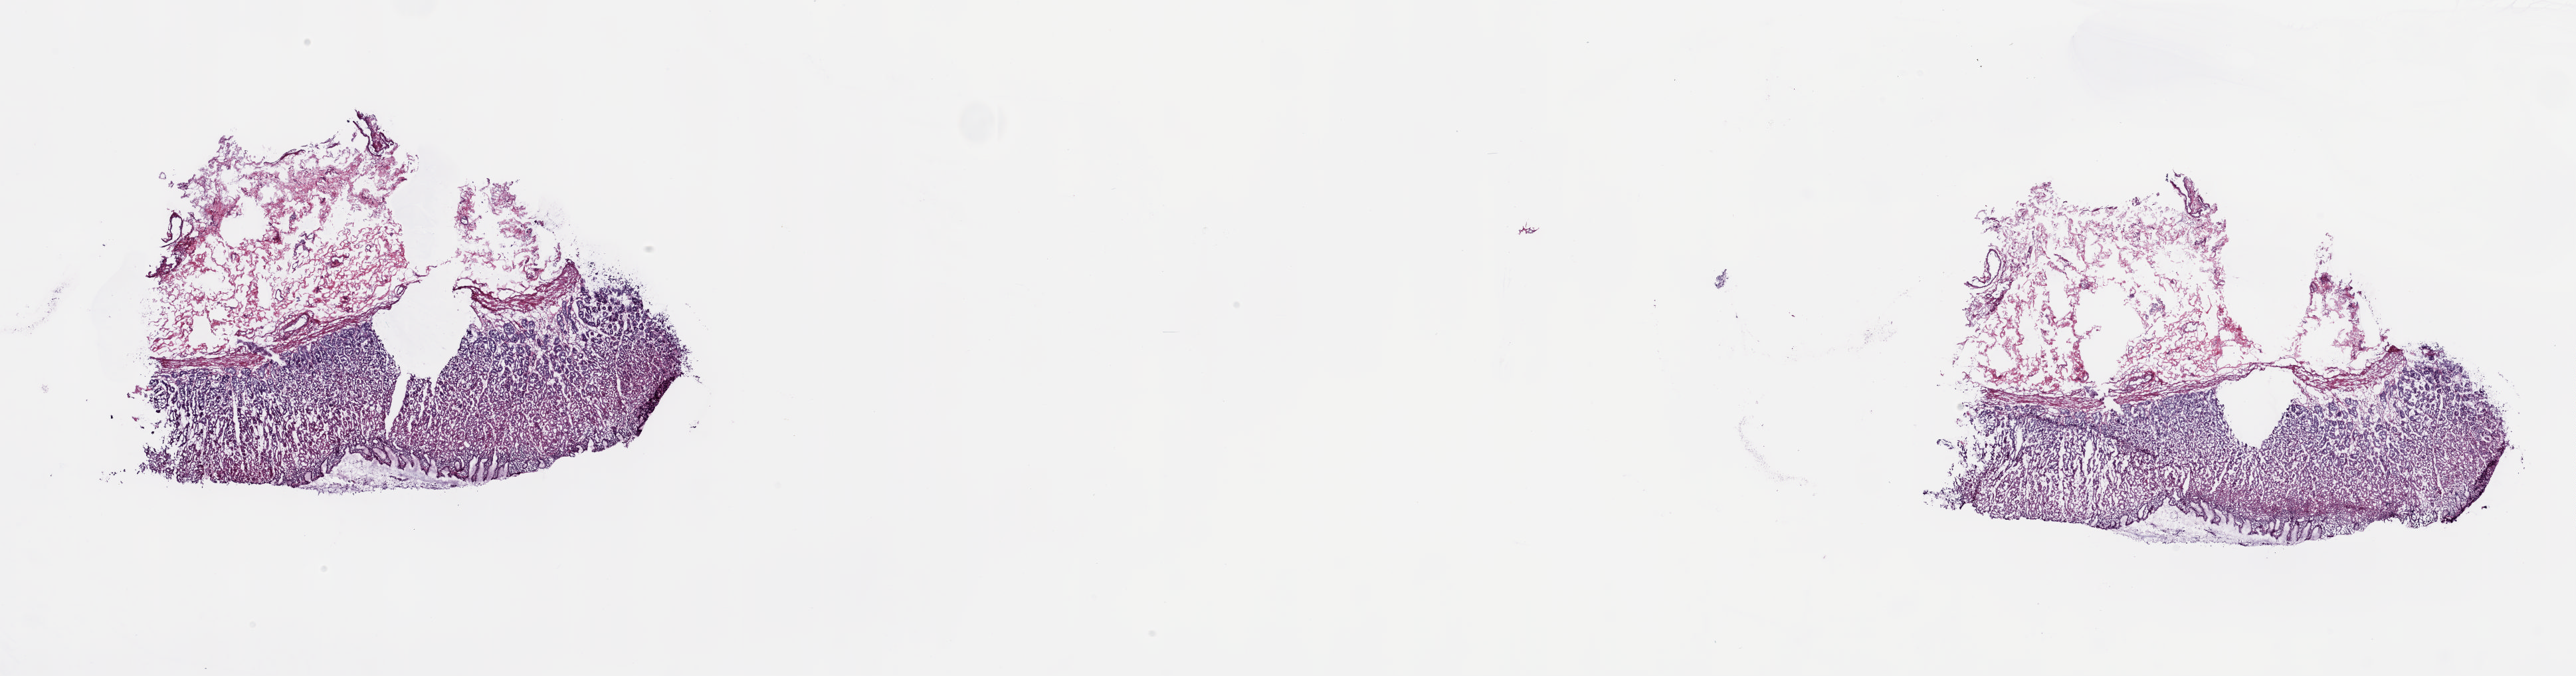
Hematoxylin and eosin (H&E) stained whole-slide image, low-resolution overview of the scanned area, about 30.7 x 8.1 mm; frozen section from the top of the tissue portion; solid tissue normal (non-tumour tissue) sample from the esophagus. Male patient; age at initial diagnosis 80 years. Pathologist review of this section (percent, as recorded): tumour cells 0%, tumour nuclei 0%, normal cells 100%, stromal cells 0%, necrosis 0%. Infiltration values recorded for this section: lymphocyte infiltration 2%, monocyte infiltration 0%, neutrophil infiltration 0%.
• this section: solid tissue normal sample (biorepository sample class)
• patient diagnosis: Adenocarcinoma, NOS (lower third of esophagus)